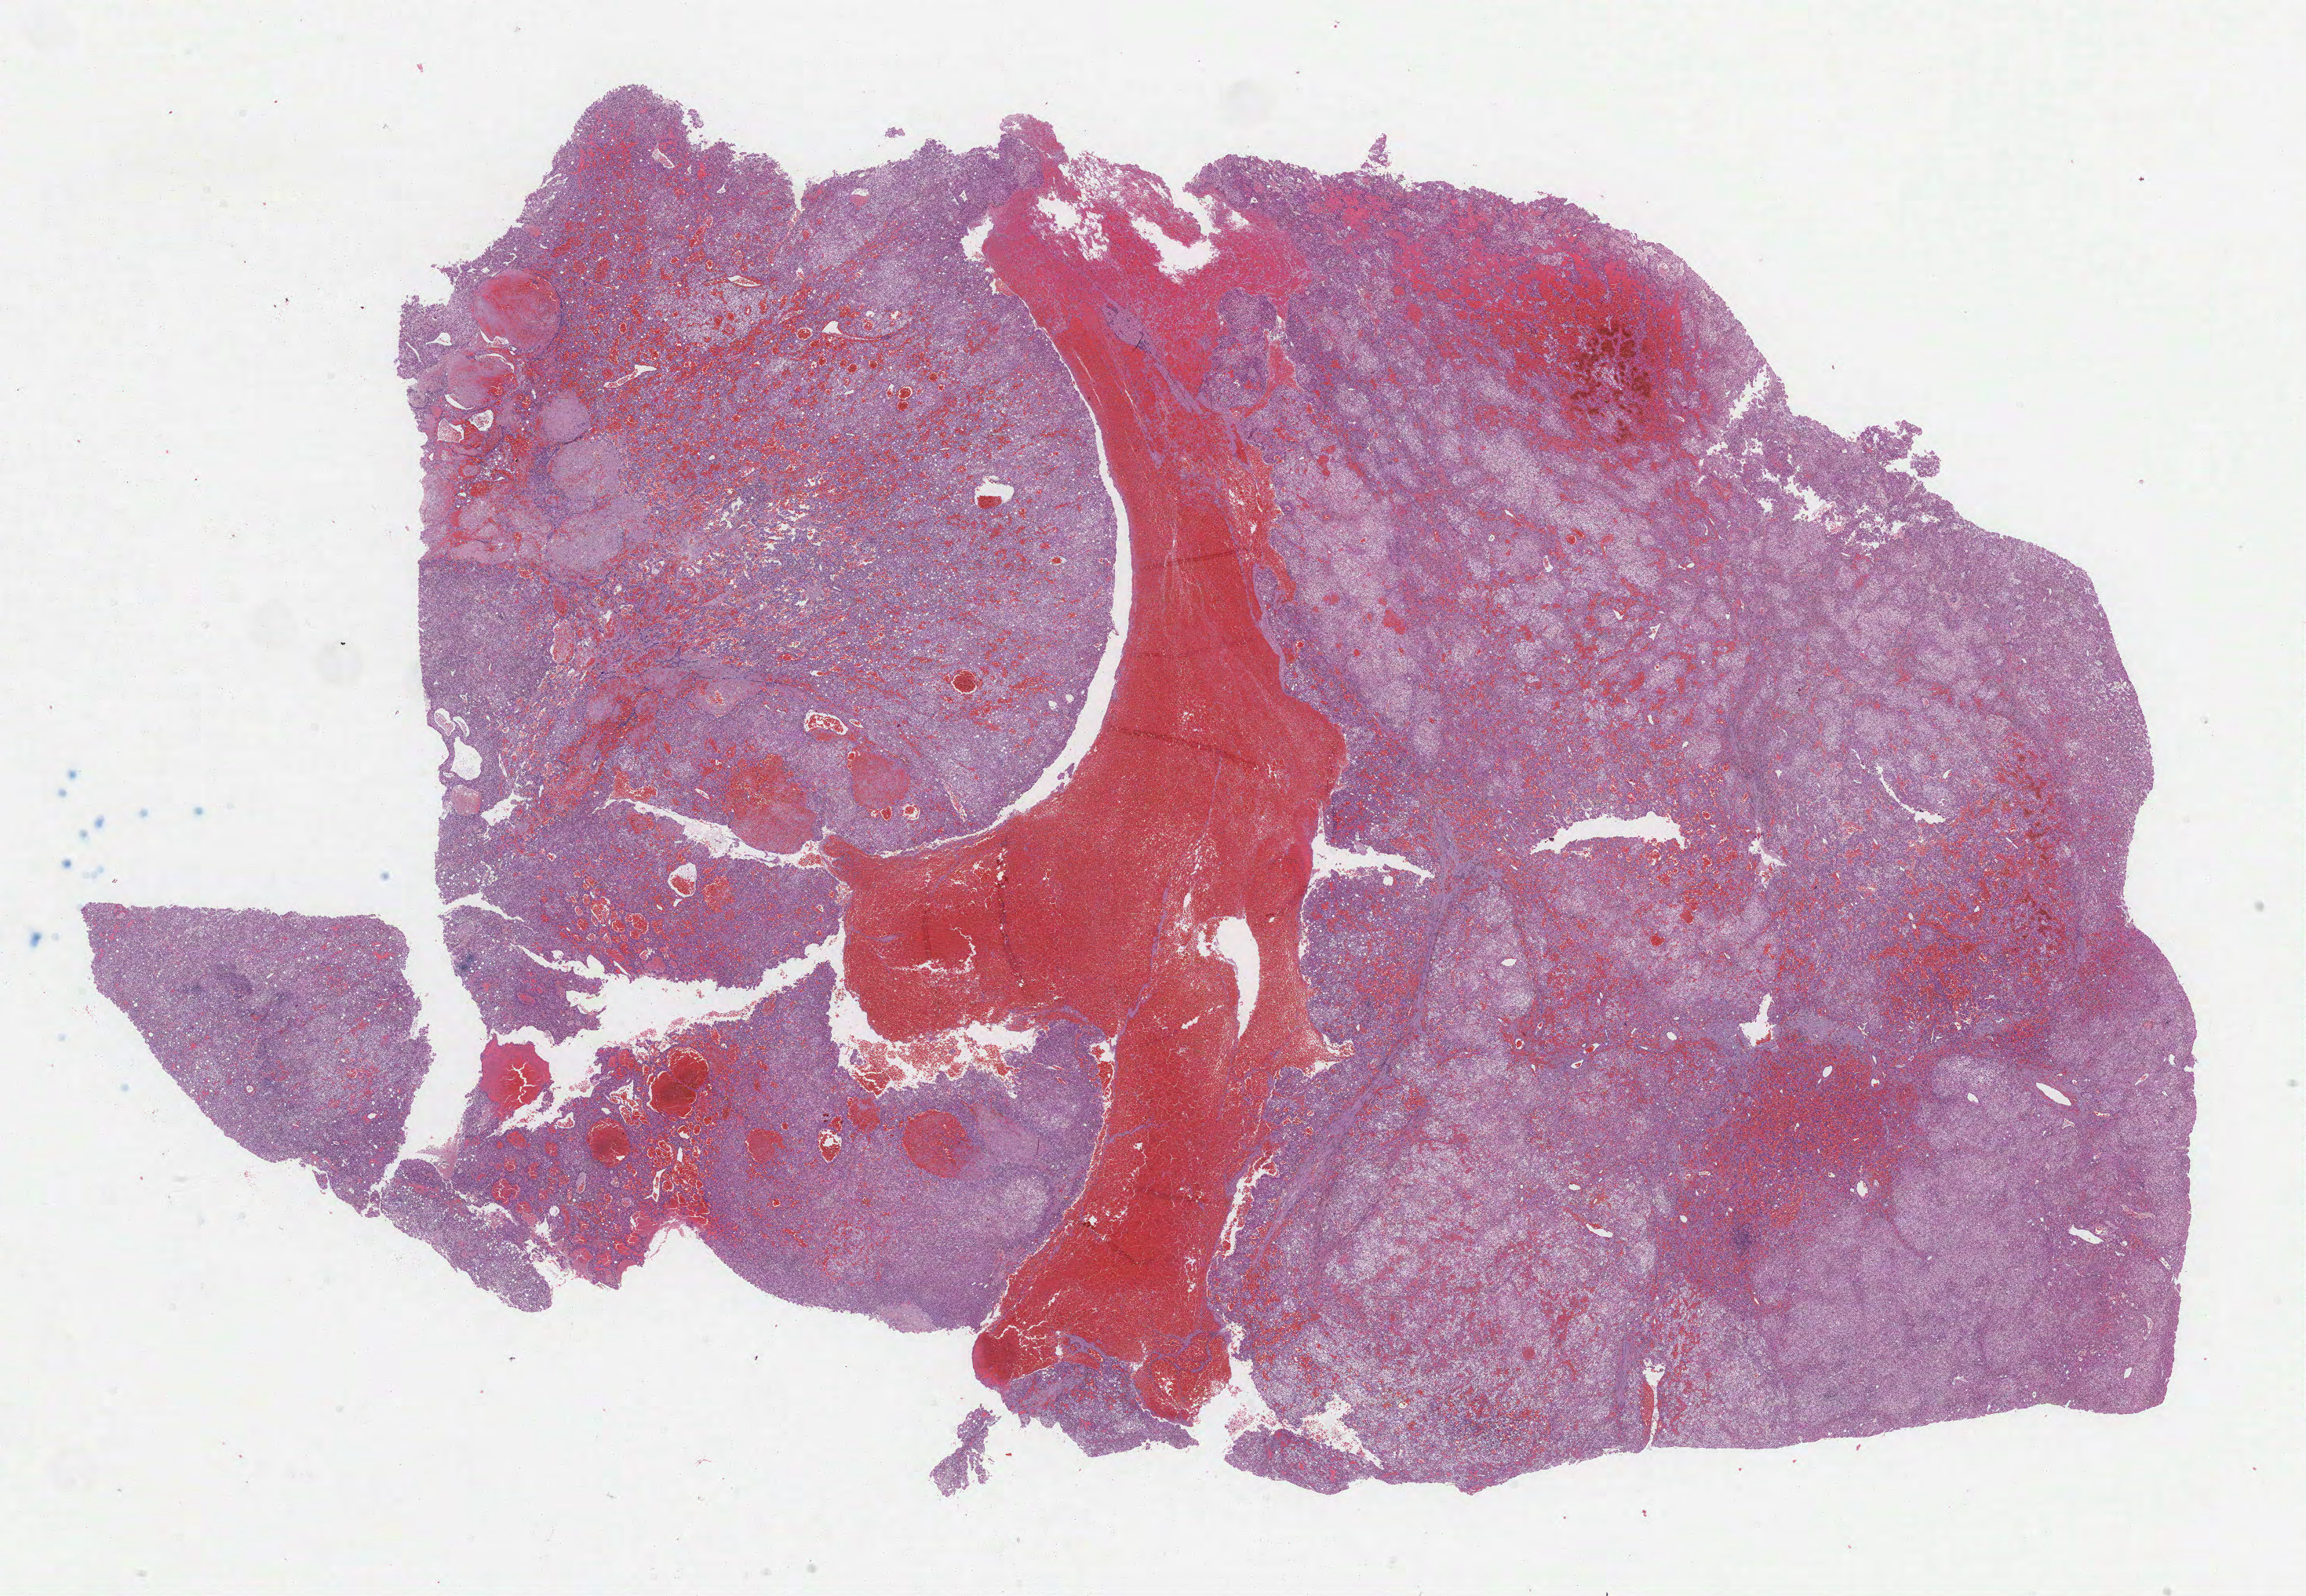
Digitized H&E-stained tissue section (whole slide) — low-resolution overview of the scanned area, about 23.7 x 16.4 mm. FFPE section. Sample: primary tumour, liver. Patient: female, age at initial diagnosis 54 years. Histologic grade: G1 (well differentiated).
AJCC pathologic stage: I. Pathologic diagnosis: Hepatocellular carcinoma, NOS.